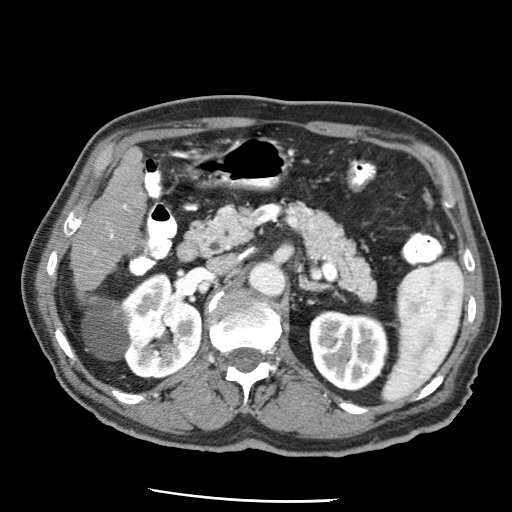
Contrast-enhanced abdominal CT (liver protocol), one axial slice. Position 17 of 79 along the scan axis. Reconstruction kernel STANDARD. Soft-tissue window (W 400 / L 40 HU). 512 × 512 image matrix, field of view 320 × 320 mm. From the clinical record (not read from this slice): diagnosis: hepatocellular carcinoma (patient treated with transarterial chemoembolisation; whether this scan precedes or follows treatment is not stated here); TNM stage (as recorded): Stage-IIIA; Child-Pugh class: A; tumour differentiation: moderately differentiated; tumour nodularity: multinodular.
Outlined on this slice (semi-automatically segmented with operator editing):
- liver parenchyma outside the tumour (the mass and vessels are separate outlines, so this box may not span the whole liver): bounding box <72,148,146,290> (left, top, right, bottom; pixels)
- liver vessels: <110,204,127,239>